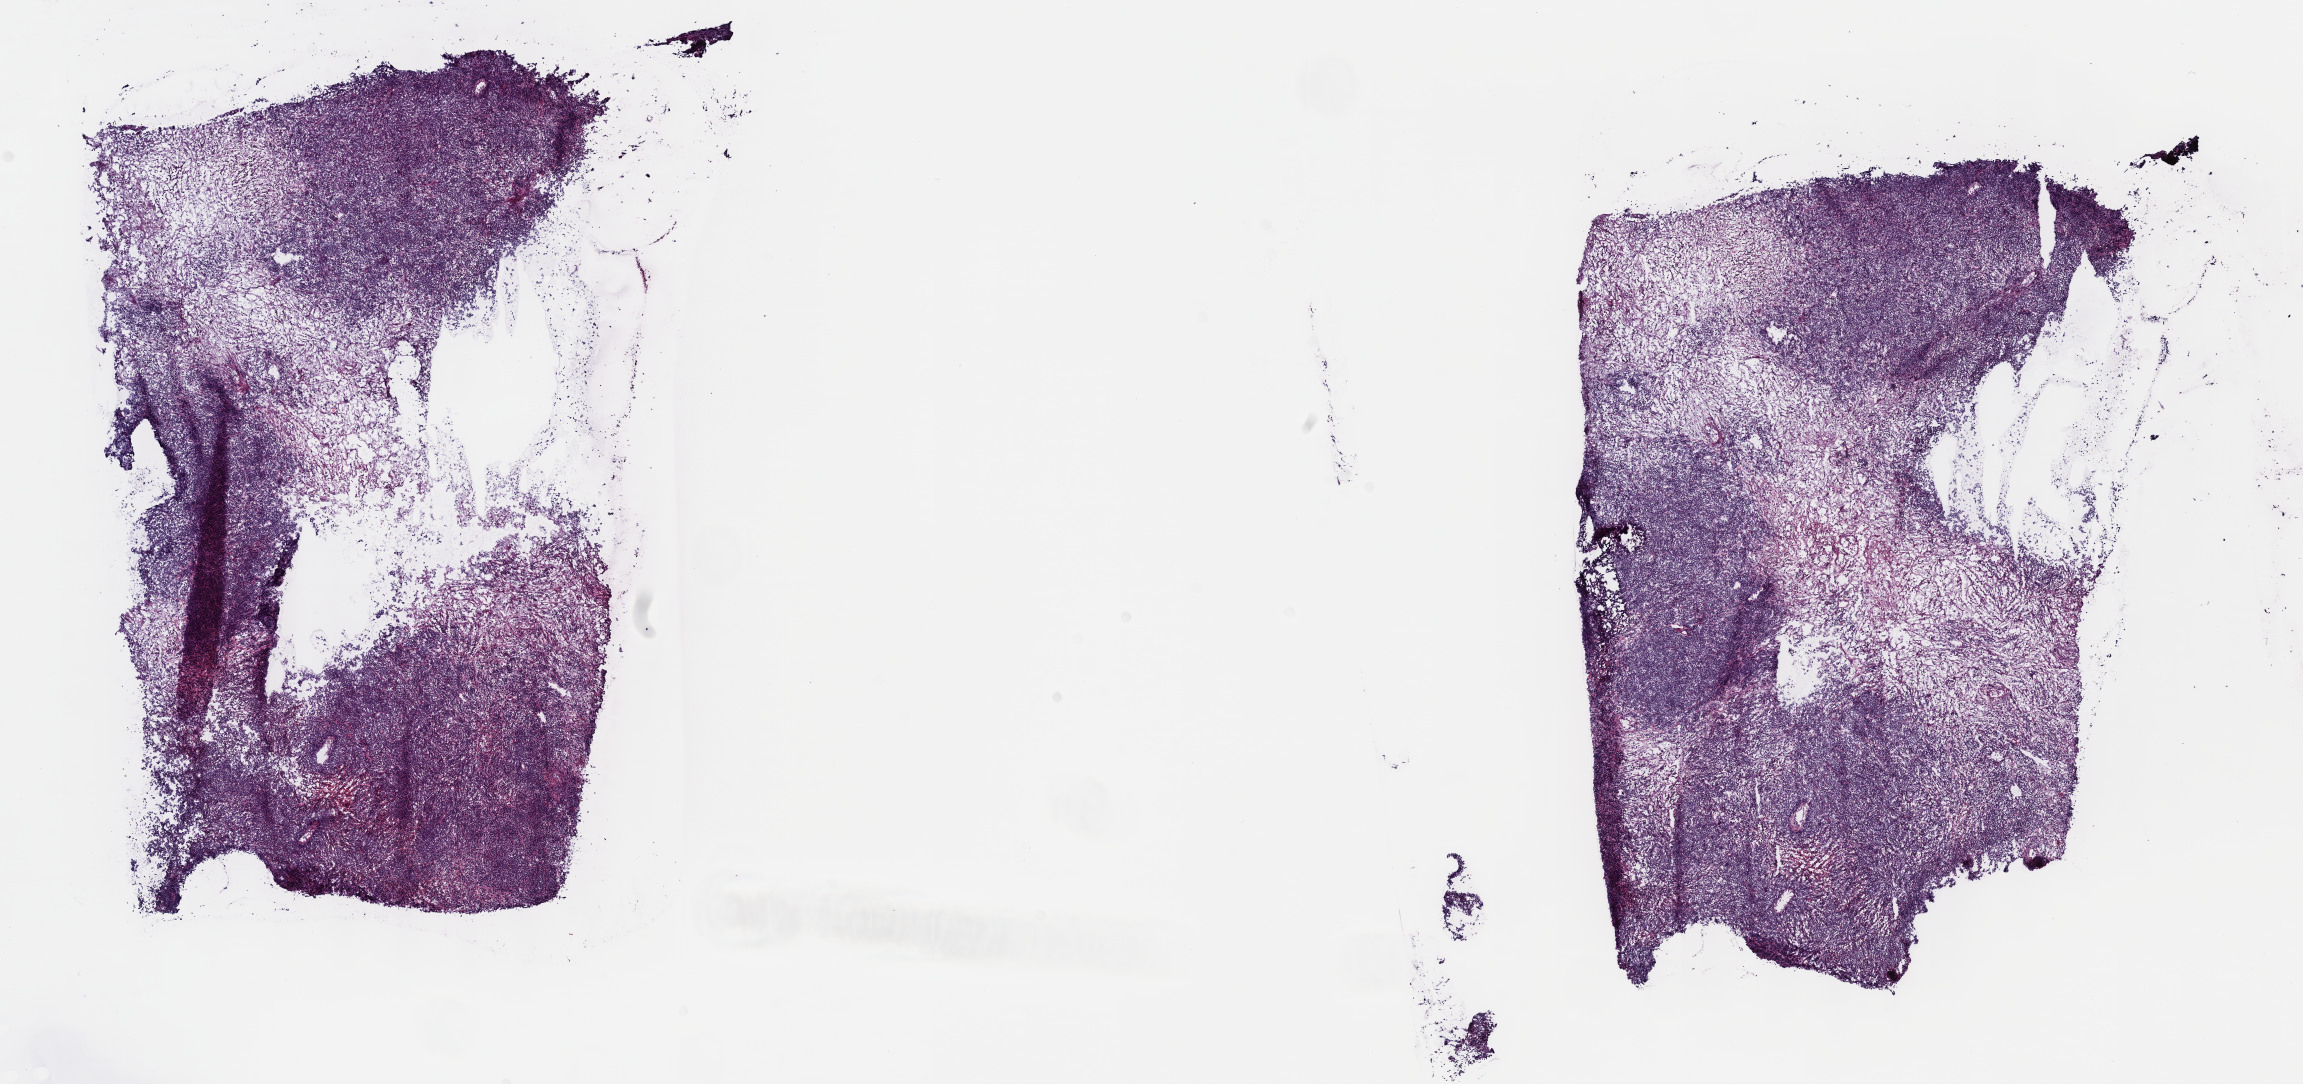
Whole-slide histology image, Hematoxylin and eosin (H&E) stained, low-resolution overview of the scanned area, about 18.6 x 8.8 mm (from a 40x scan), frozen section from the top of the tissue portion, sample: primary tumour, lymphoid tissue. Patient: male, age at initial diagnosis 70 years. Slide review estimates, as recorded: tumour cells 60%, tumour nuclei 80%, normal cells 5%, stromal cells 30%, necrosis 5%. Infiltration values recorded for this section: lymphocyte infiltration 60%, monocyte infiltration 10%, neutrophil infiltration 10%.
• histologic diagnosis: Diffuse large B-cell lymphoma, NOS